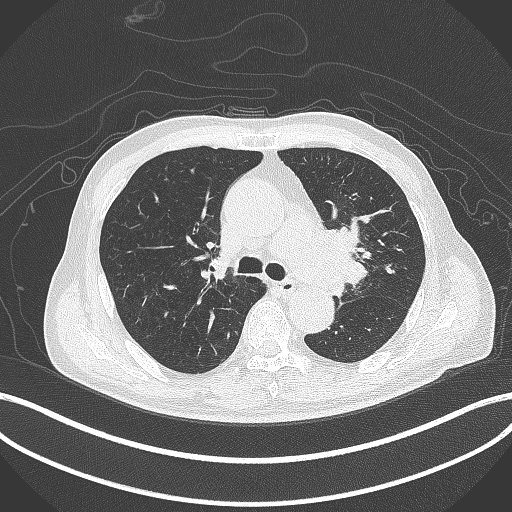
Chest CT, one axial slice. Slice 281 of 417 in the series (ordered by position). 120 kVp. Lung window (W 1500 / L -600 HU). 1 mm slice thickness. 512 × 512 image matrix, field of view 400 × 400 mm. Male patient, age 77 years. Case-level facts recorded for this patient, not image findings: clinical TNM (as recorded): T3 N1 M0.
Annotated regions visible in this slice (bounding box drawn by a radiologist):
- lung tumour (recorded histology: adenocarcinoma): box from (x=316, y=220) to (x=370, y=296) px